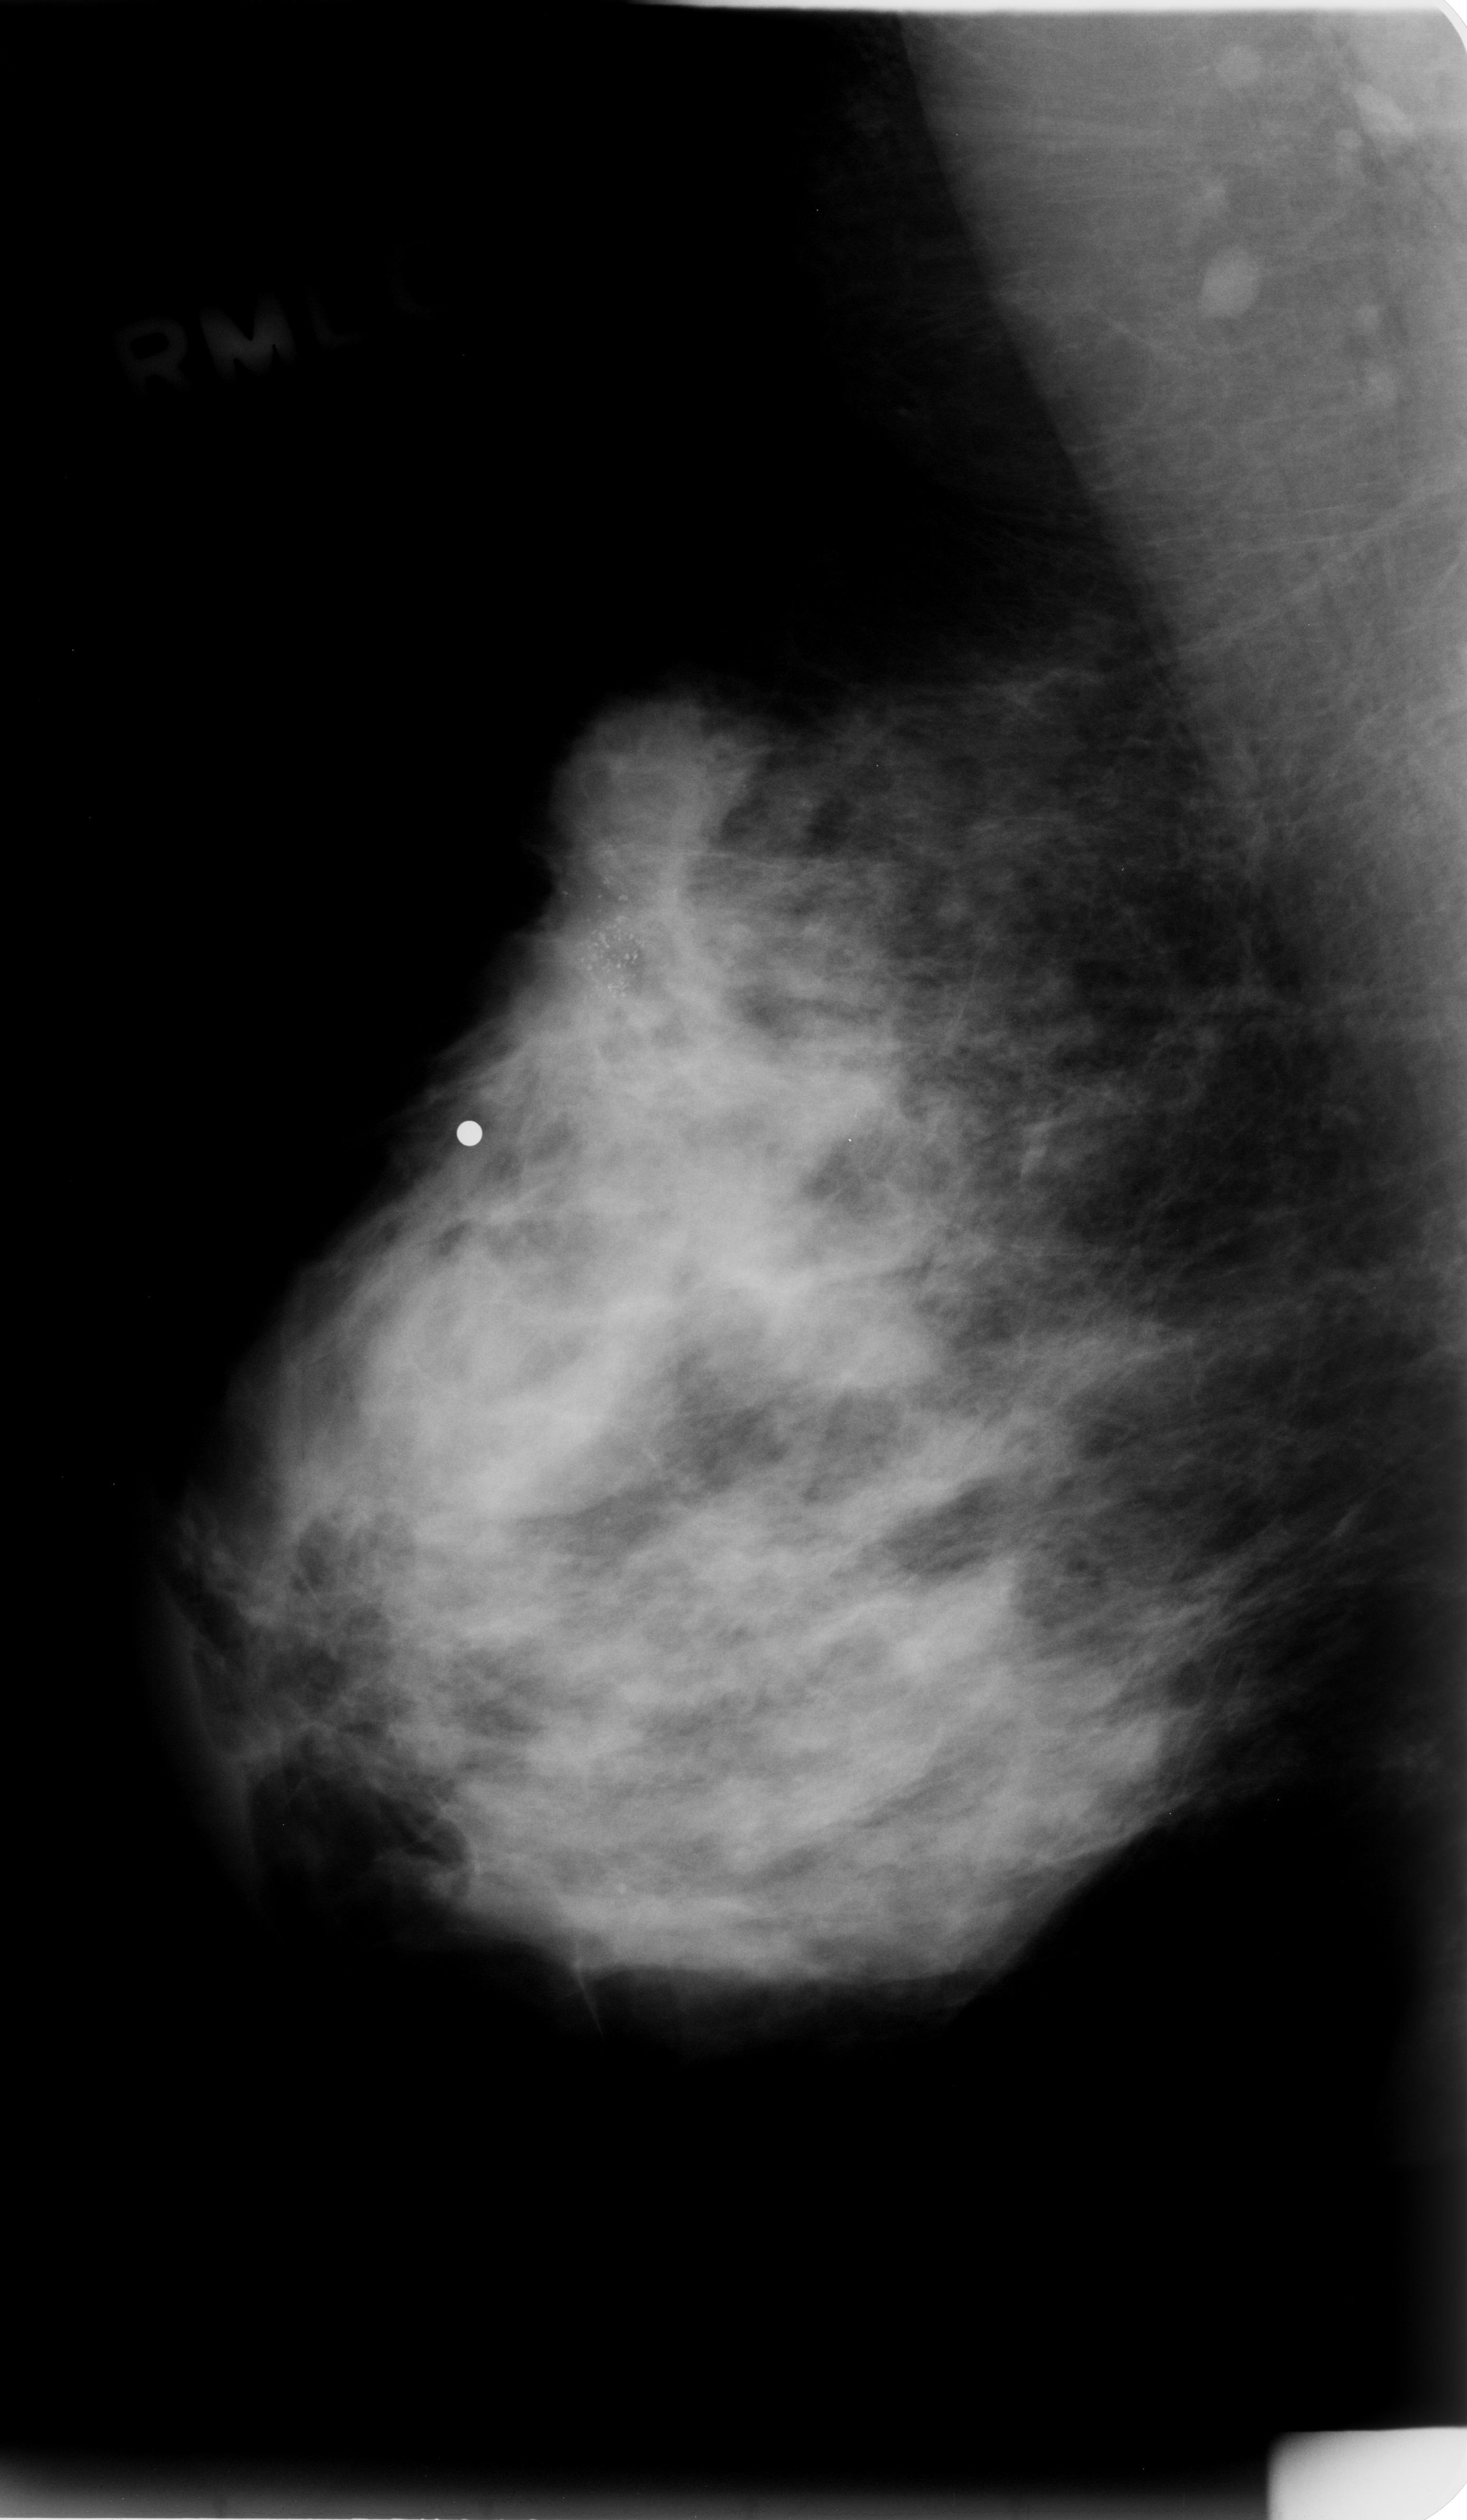
Mammogram (digitized film). Right breast. MLO view. BI-RADS breast density category 3 (scale 1–4). 1467 × 2520 image matrix.
Marked abnormalities (boxes around the expert regions of interest):
- calcifications, morphology pleomorphic, distribution clustered; BI-RADS assessment category 5; subtlety rating 5 on a 1 (subtle) to 5 (obvious) scale; pathology result (as recorded, not read from the image): malignant: box from (x=503, y=638) to (x=847, y=1126) px